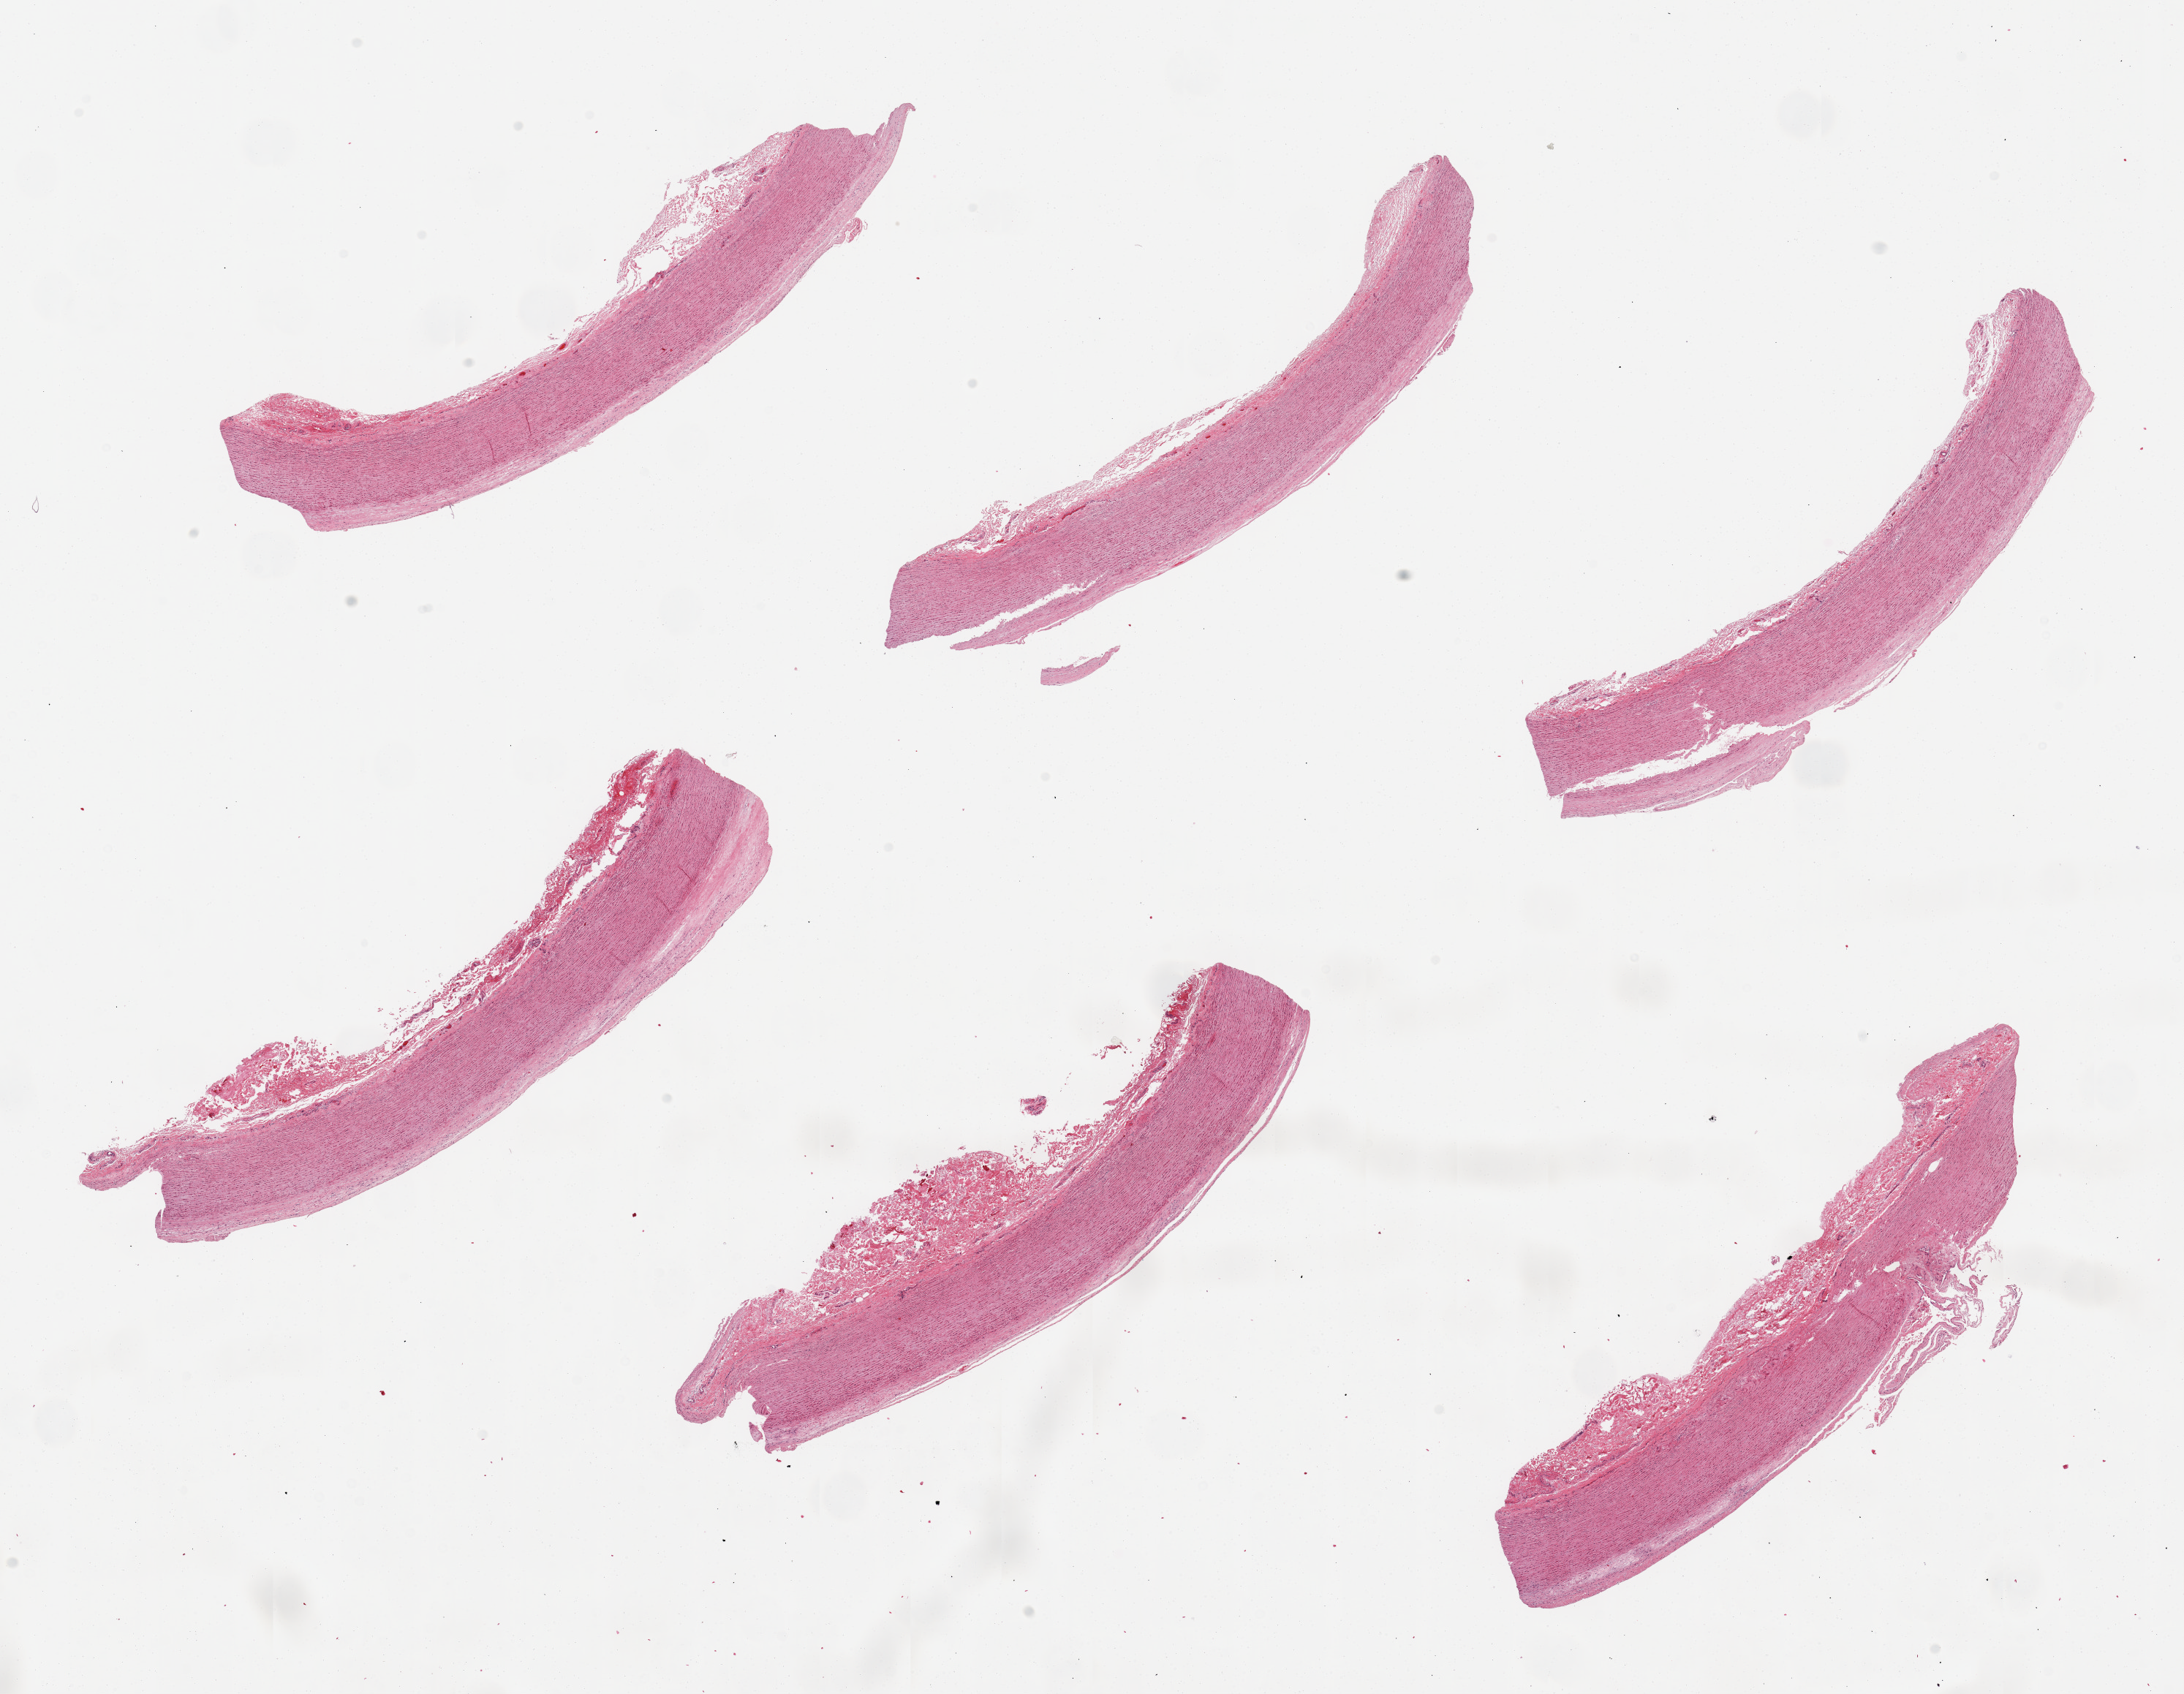
Whole-slide image, haematoxylin and eosin stain, a low-resolution overview of the entire scanned area, about 23.6 x 18.3 mm, PAXgene-fixed paraffin-embedded (PFPE) section, section of aorta (target tissue), tissue donor sample.
Pathologist's review note for this sample: 6 pieces, mild atherosis (~0.2mm); adherent serosa up to ~0.5mm.